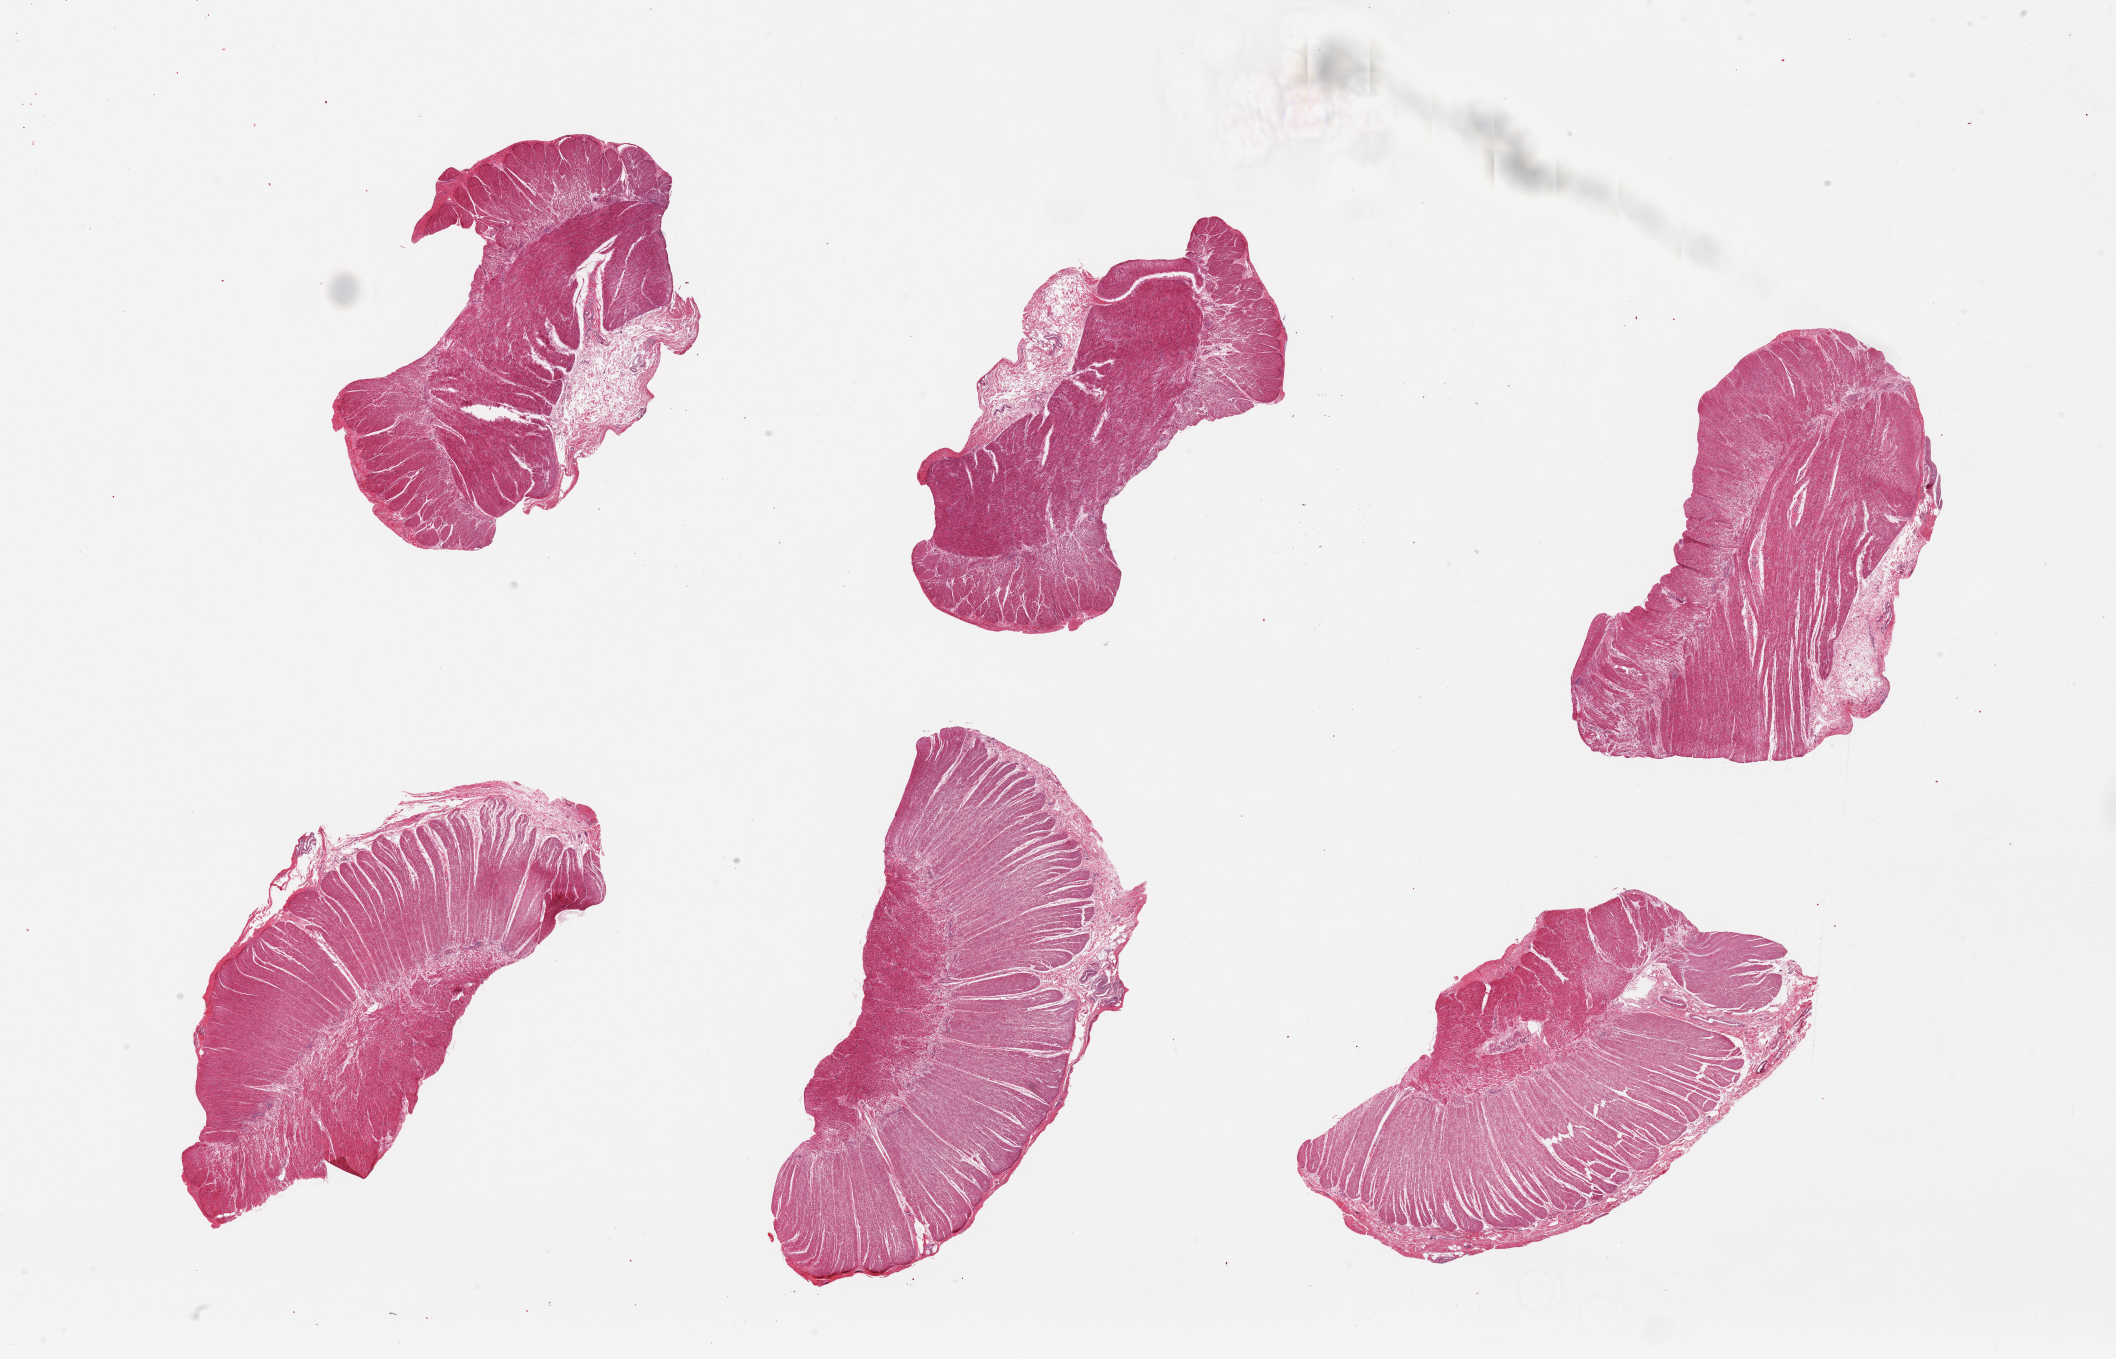
Whole-slide image, haematoxylin and eosin stain — low-resolution overview of the scanned area, about 33.5 x 21.5 mm, PAXgene-fixed, paraffin-embedded tissue, section of sigmoid colon (target tissue), tissue donor sample. Female donor.
Pathologist's review note for this sample: 6 pieces, up to 9x5mm; generally all muscularis.